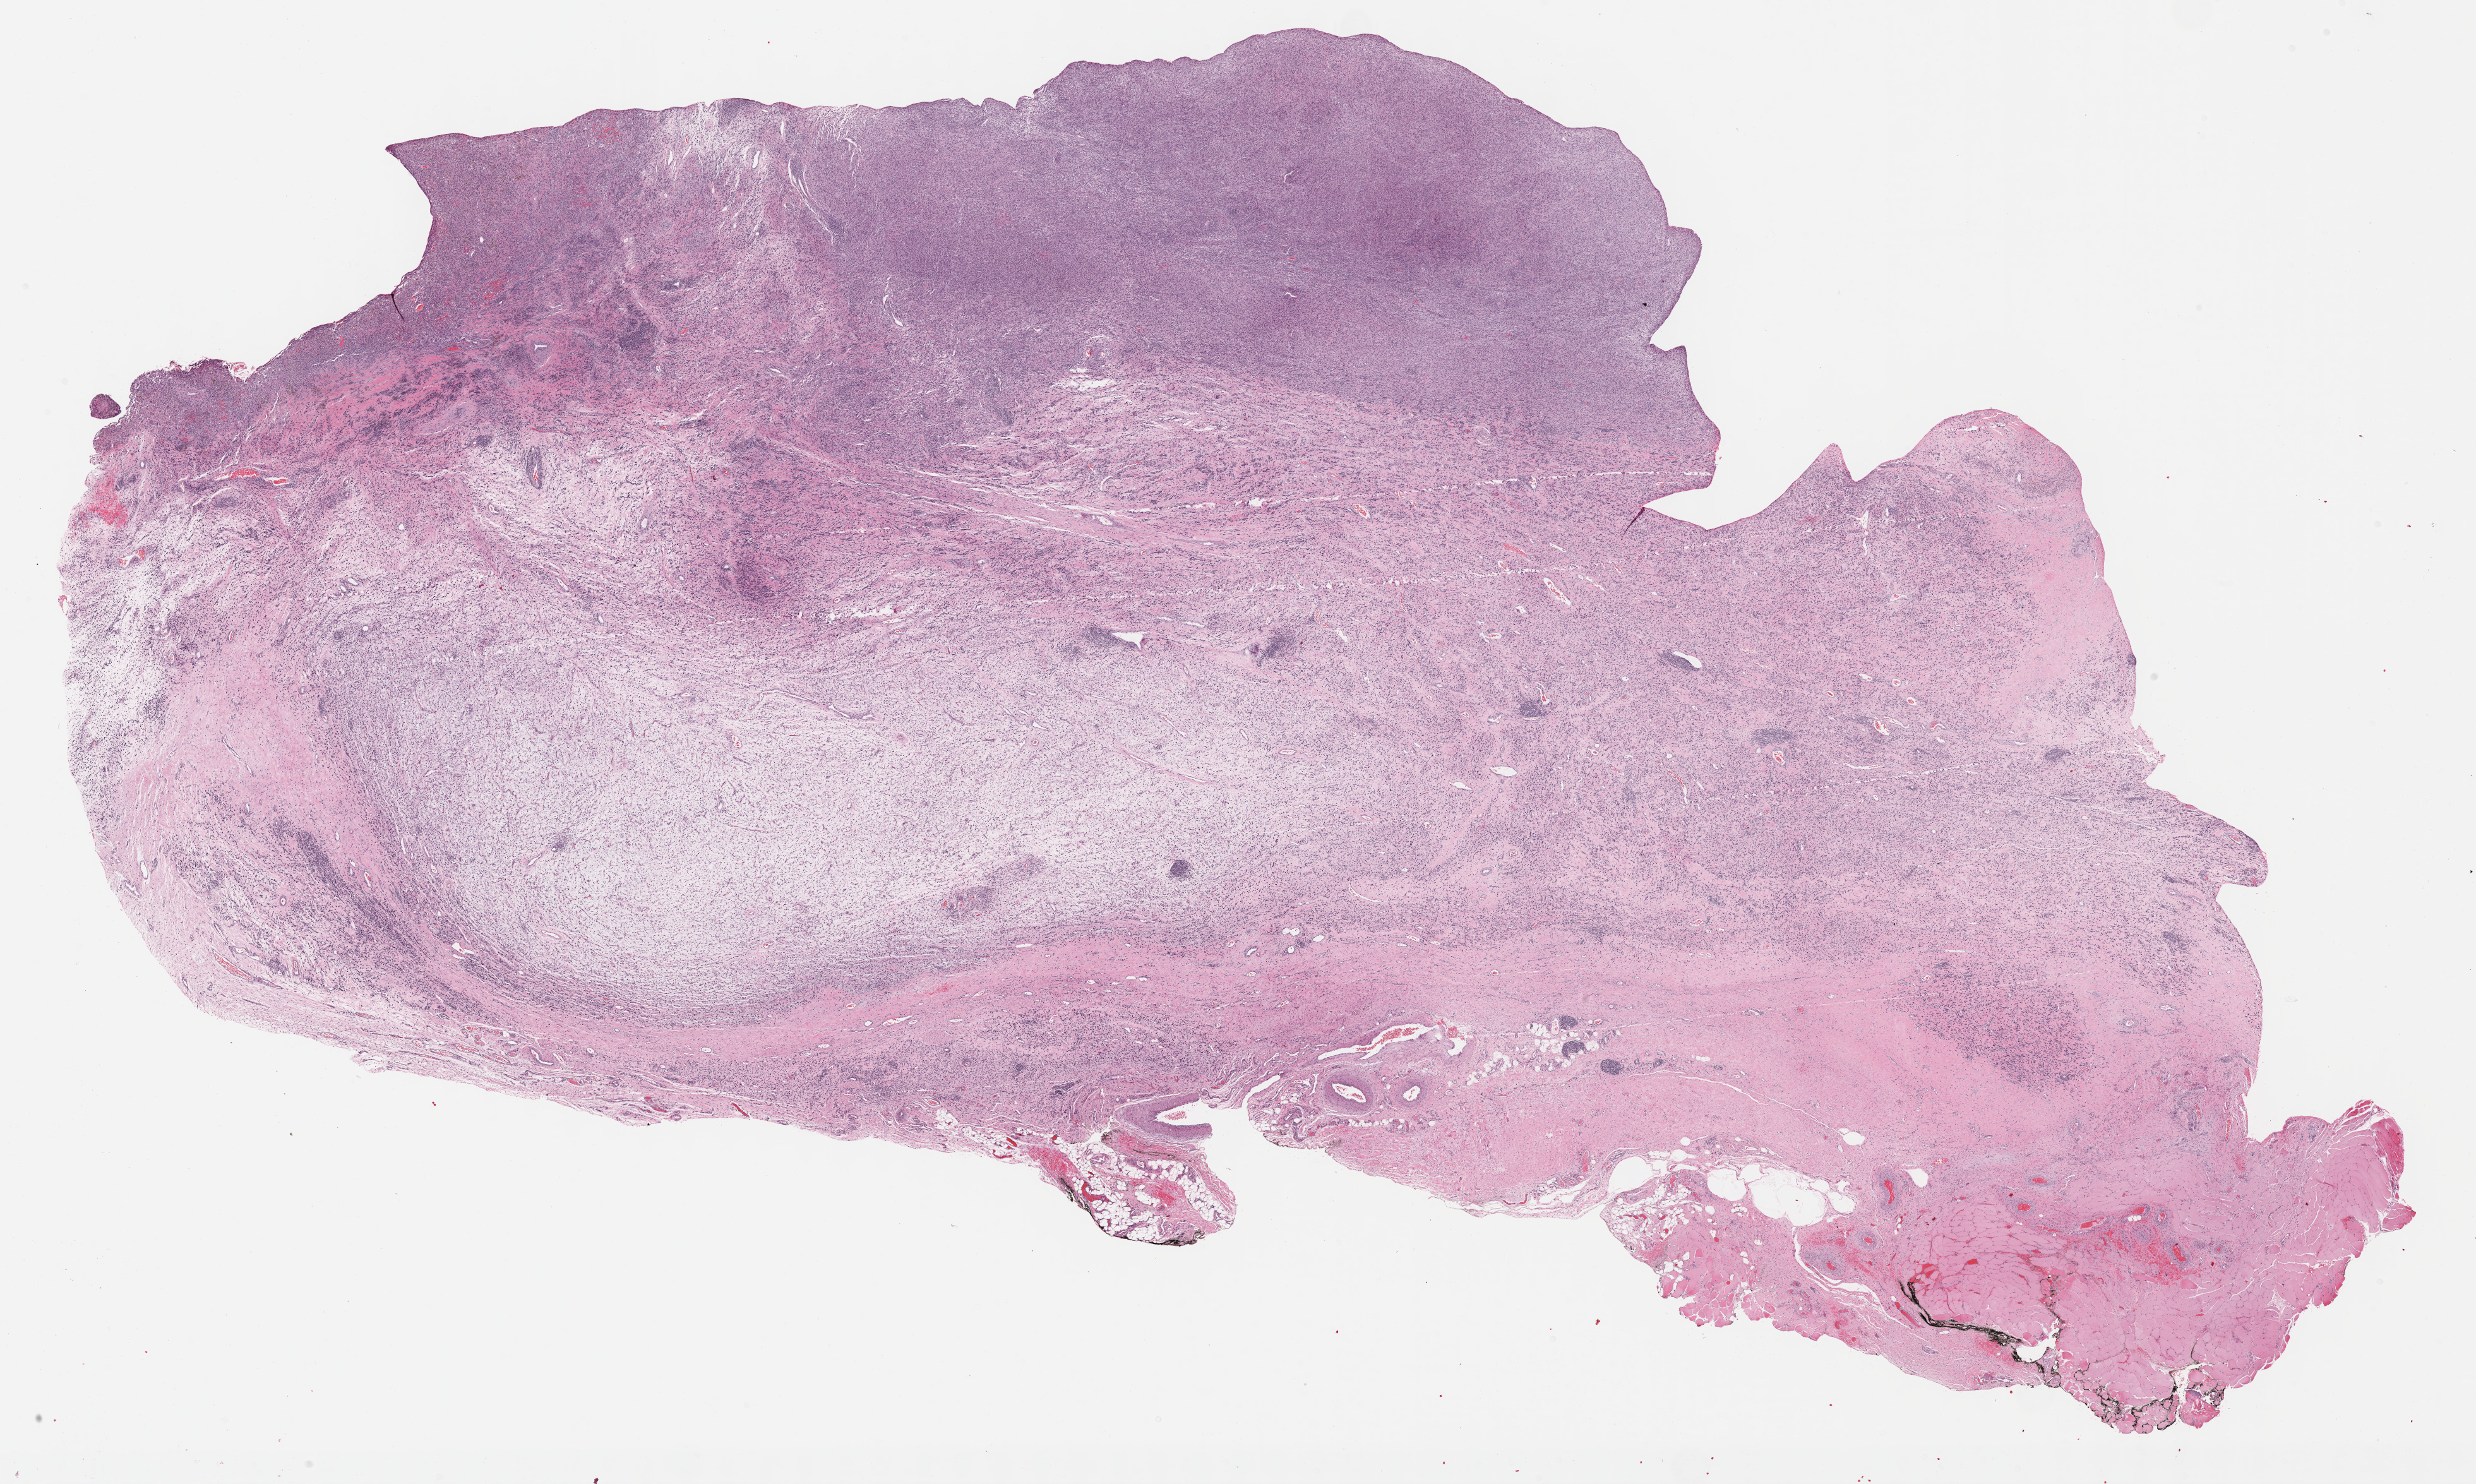
Digitized Hematoxylin and eosin (H&E) stained tissue section (whole slide), low-resolution overview of the scanned area, about 31.7 x 19.0 mm (acquisition: 40x scan). Formalin-fixed paraffin-embedded (FFPE) diagnostic section. Primary tumour sample from the connective, subcutaneous and other soft tissues. Patient: male, age at initial diagnosis 62 years.
Histologic diagnosis: Dedifferentiated liposarcoma.